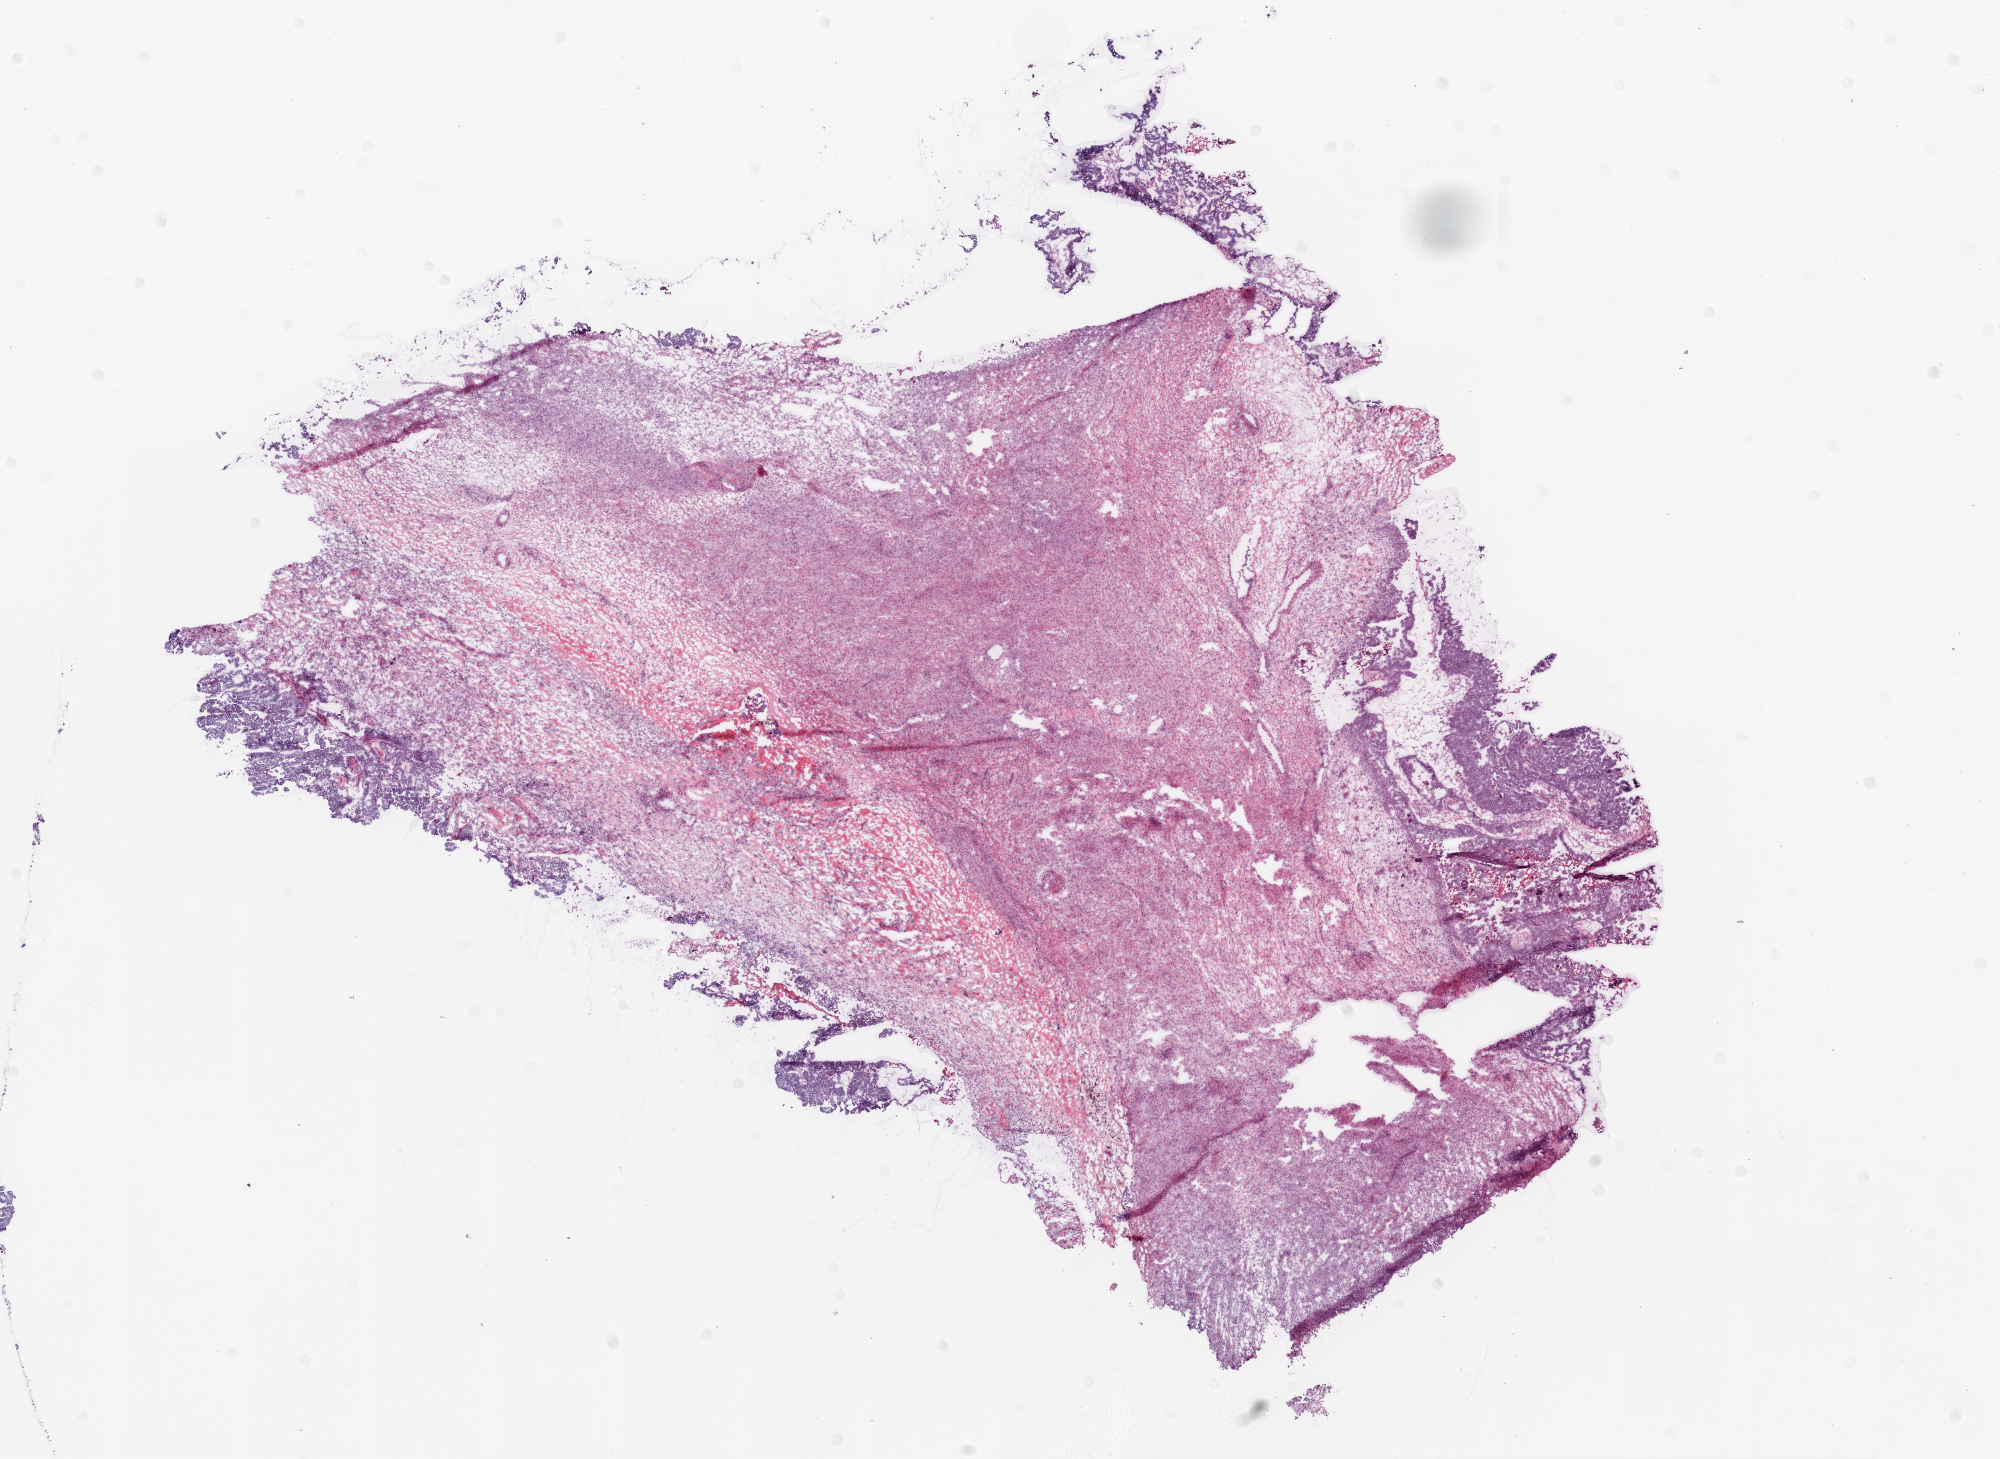
H&E whole-slide image — a low-resolution overview of the entire scanned area, about 16.0 x 11.7 mm. Frozen section. Primary tumour sample from the ovary. Female patient; age at initial diagnosis 76 years. Histologic grade: G2 (moderately differentiated). Composition of this section per pathologist review: tumour cells 13%, tumour nuclei 85%, normal cells 0%, stromal cells 85%, necrosis 2%.
- histologic diagnosis: Serous cystadenocarcinoma, NOS
- laterality: bilateral
- FIGO stage: IIIC